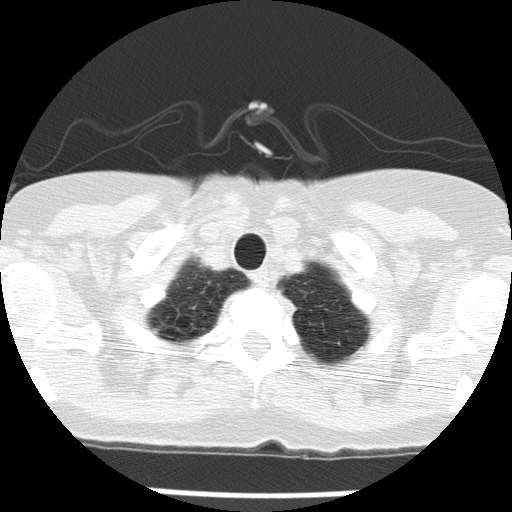
Low-dose screening chest CT, one axial slice. Slice 132 of 143 in the series (ordered by position). Reconstruction kernel FC51. Lung window (W 1500 / L -600 HU). 2 mm slice thickness. 512 × 512 image matrix, field of view 276 × 276 mm.
Structures marked on this image (expert manual segmentation):
- lesion 1 (tumor, upper lobe of left lung): bounding box [x1, y1, x2, y2] px = [277, 289, 297, 316]